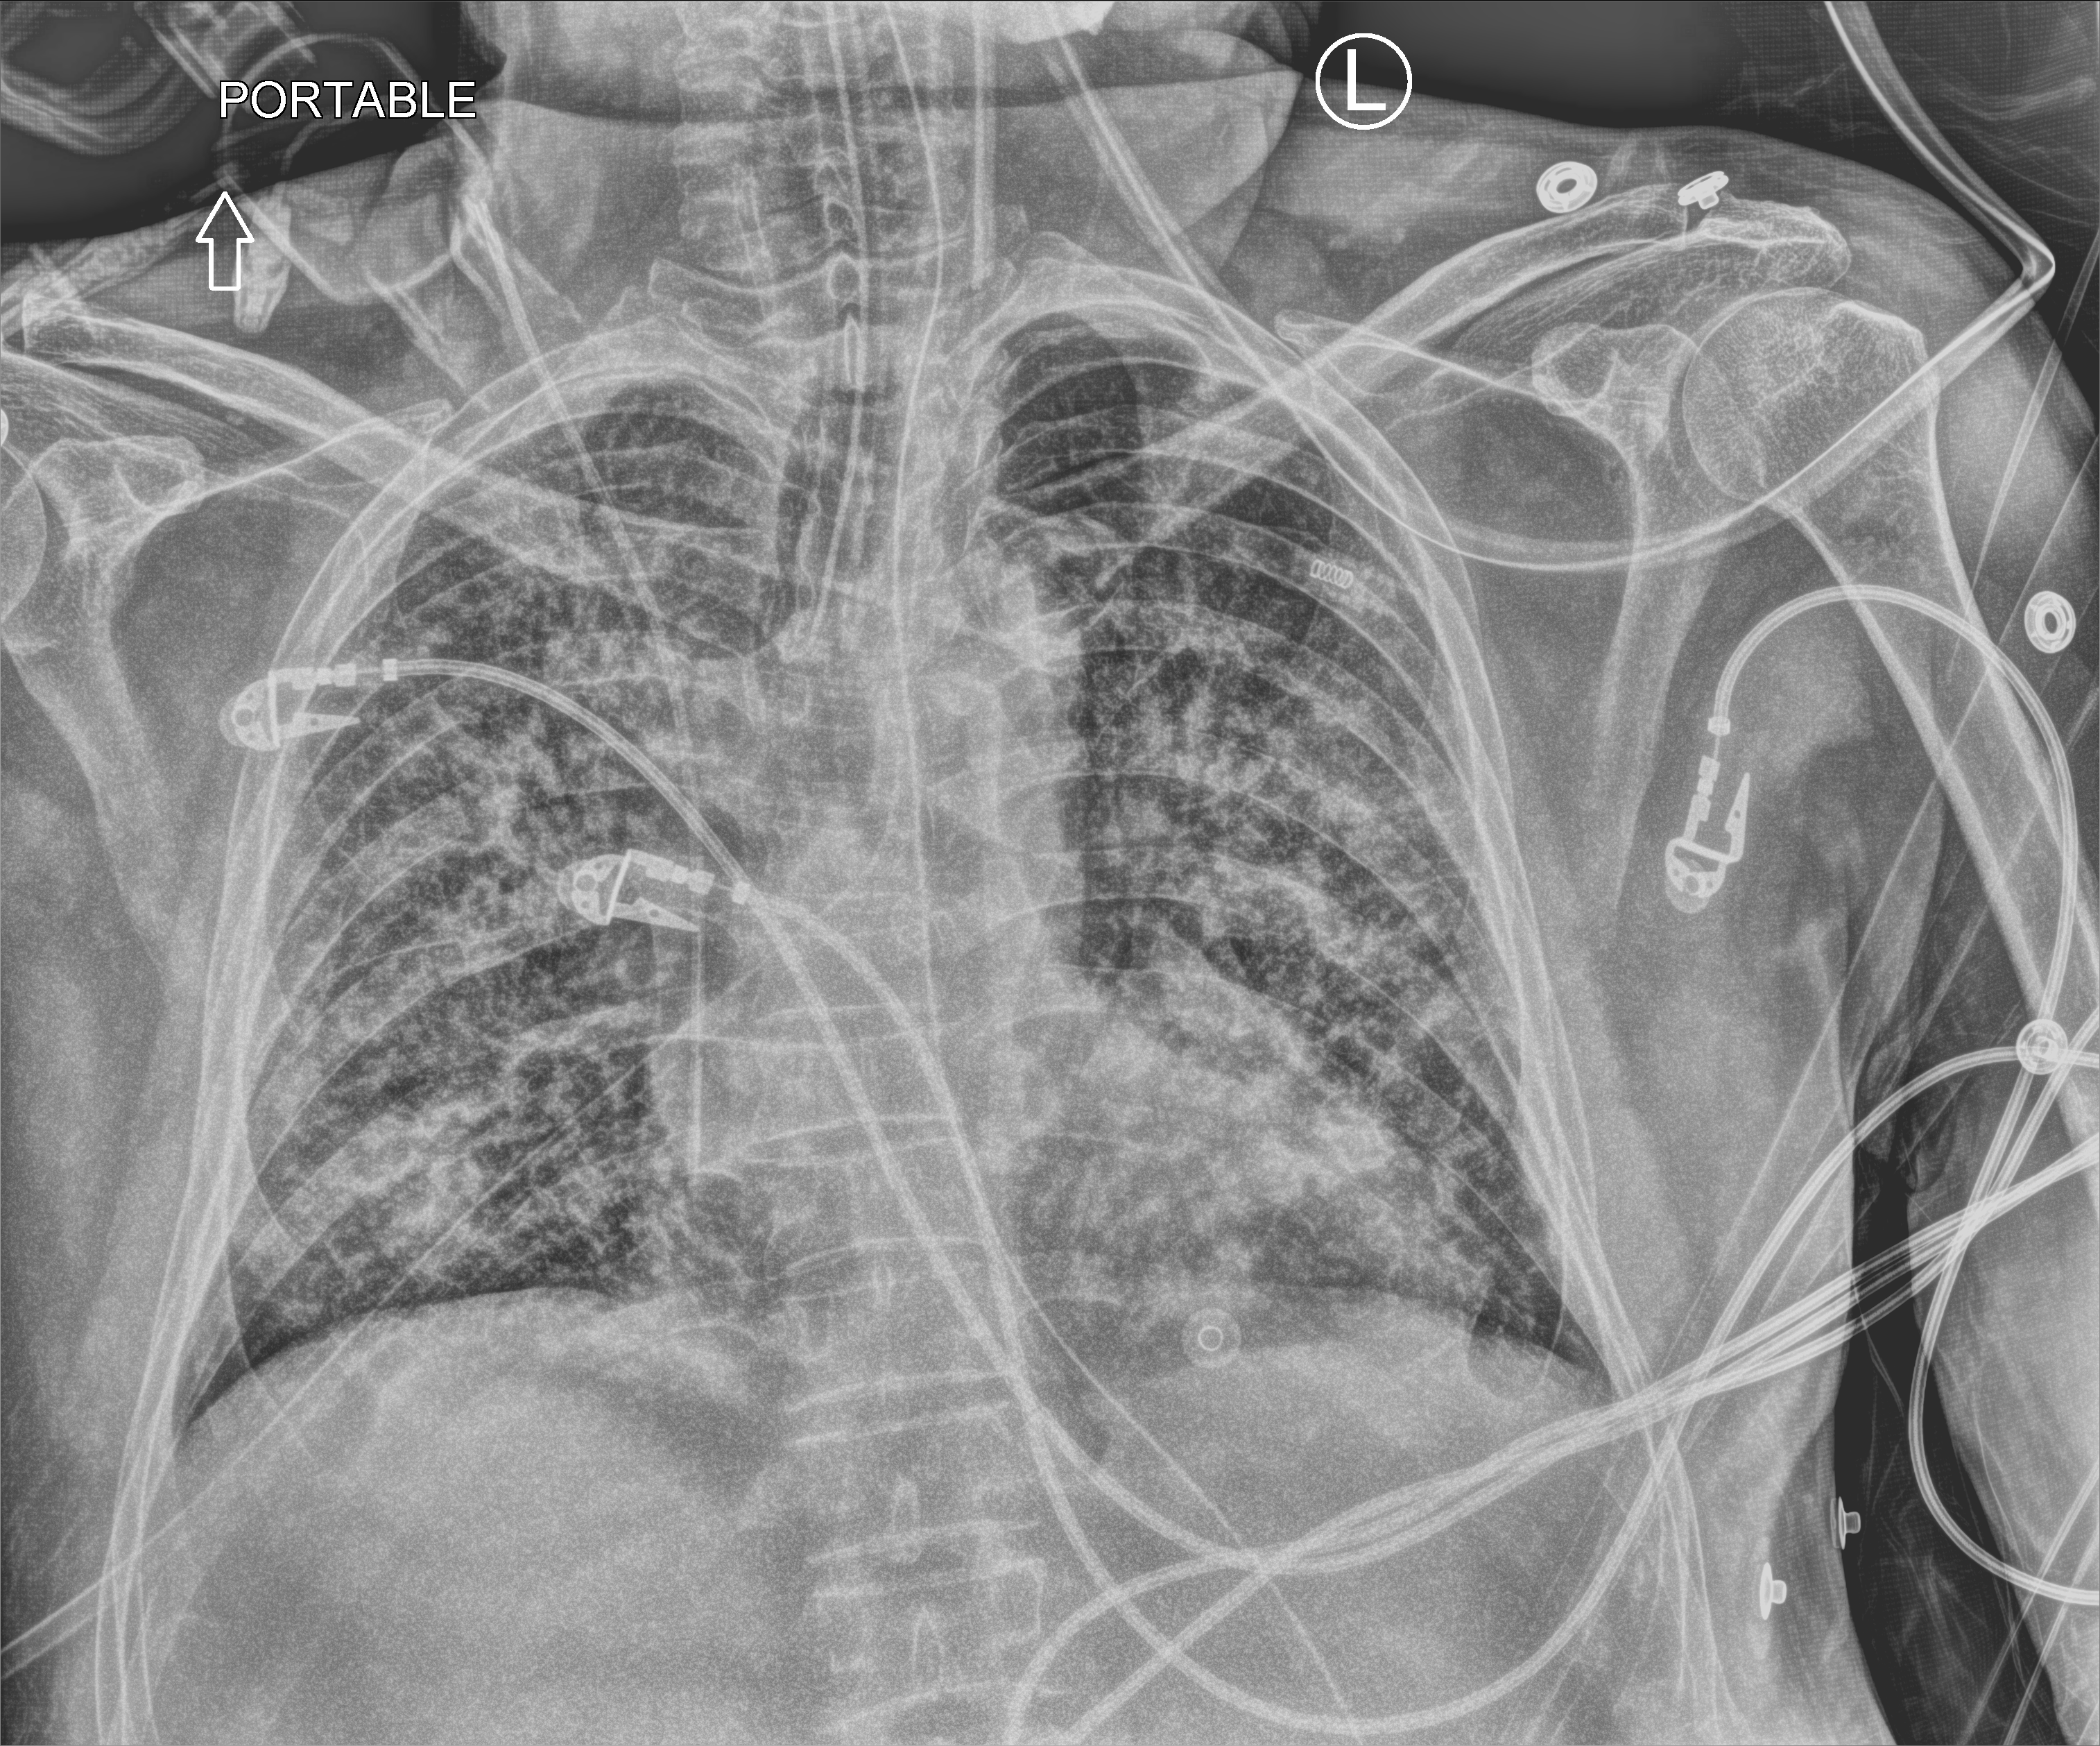
Chest X-ray (portable), anteroposterior (AP) projection. Patient hospitalised with COVID-19; male, aged 60–74 years.
From the hospital-stay record, not from the radiograph (when in the stay this image was taken is not recorded):
- admitted to intensive care during this hospital stay: yes